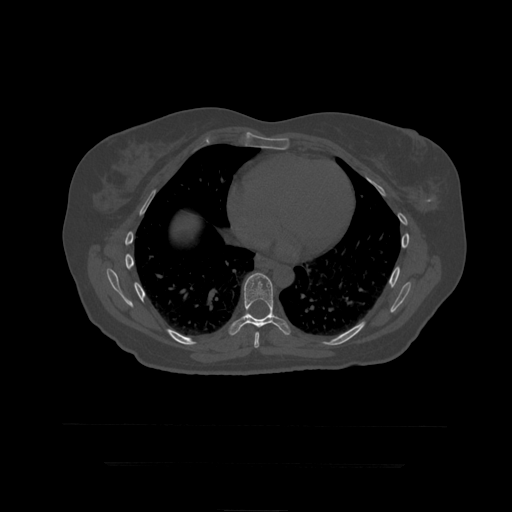
CT including the spine, one axial slice. Slice 264 of 399 in the series (ordered by position). Reconstruction kernel STANDARD. 120 kVp. Bone window (W 1800 / L 400 HU). 1.25 mm slice thickness. 512 × 512 image matrix, field of view 450 × 450 mm. Patient age 41 years. From the clinical record (not read from this slice): primary cancer: breast.
Outlined on this slice (semi-automatic segmentation, software-assisted and operator-edited):
- T8 vertebra: bounding box (x1, y1, x2, y2) in pixels: (254, 332, 260, 348)
- T9 vertebra: (229, 273, 291, 336)